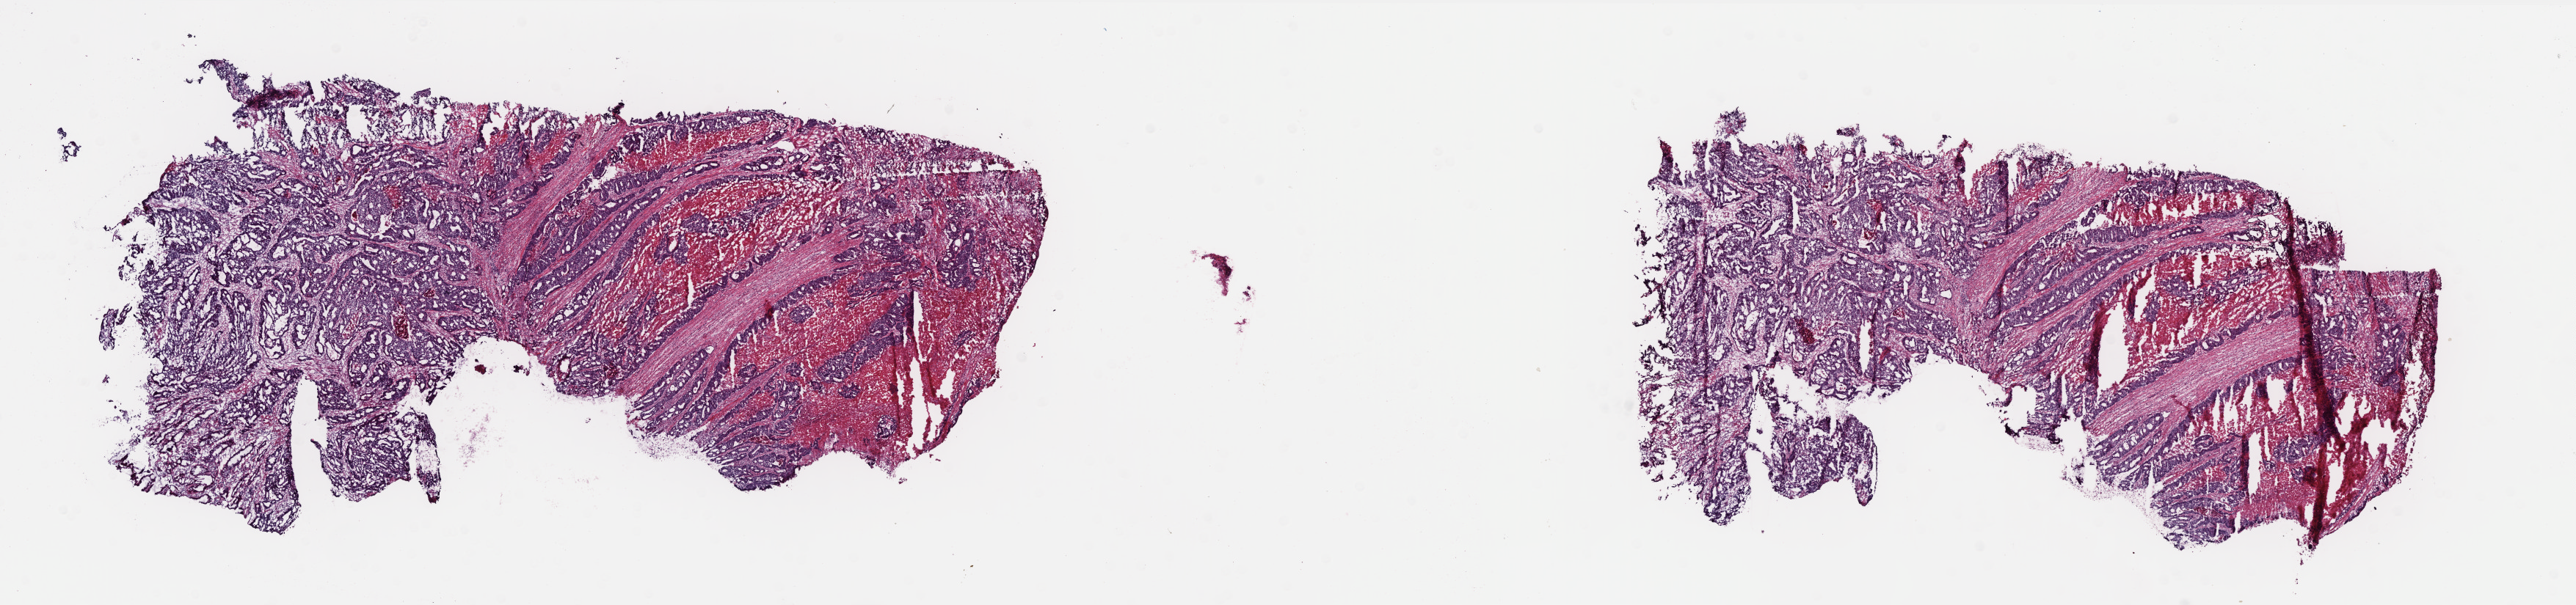
Hematoxylin and eosin (H&E) stained whole-slide image, whole scanned area (about 28.1 x 6.6 mm, from a 40x scan) shown as a low-resolution overview; frozen section from the bottom of the tissue portion; sample: primary tumour, colon. Female patient; age at initial diagnosis 68 years. Composition of this section per pathologist review: tumour cells 55%, tumour nuclei 85%, normal cells 10%, stromal cells 10%, necrosis 25%. Inflammatory infiltration, as recorded: lymphocyte infiltration 1%, monocyte infiltration 0%, neutrophil infiltration 1%.
AJCC pathologic stage: IV (6th edition). Pathologic diagnosis: Carcinoma, NOS (sigmoid colon). TNM: T3 N1 M1.